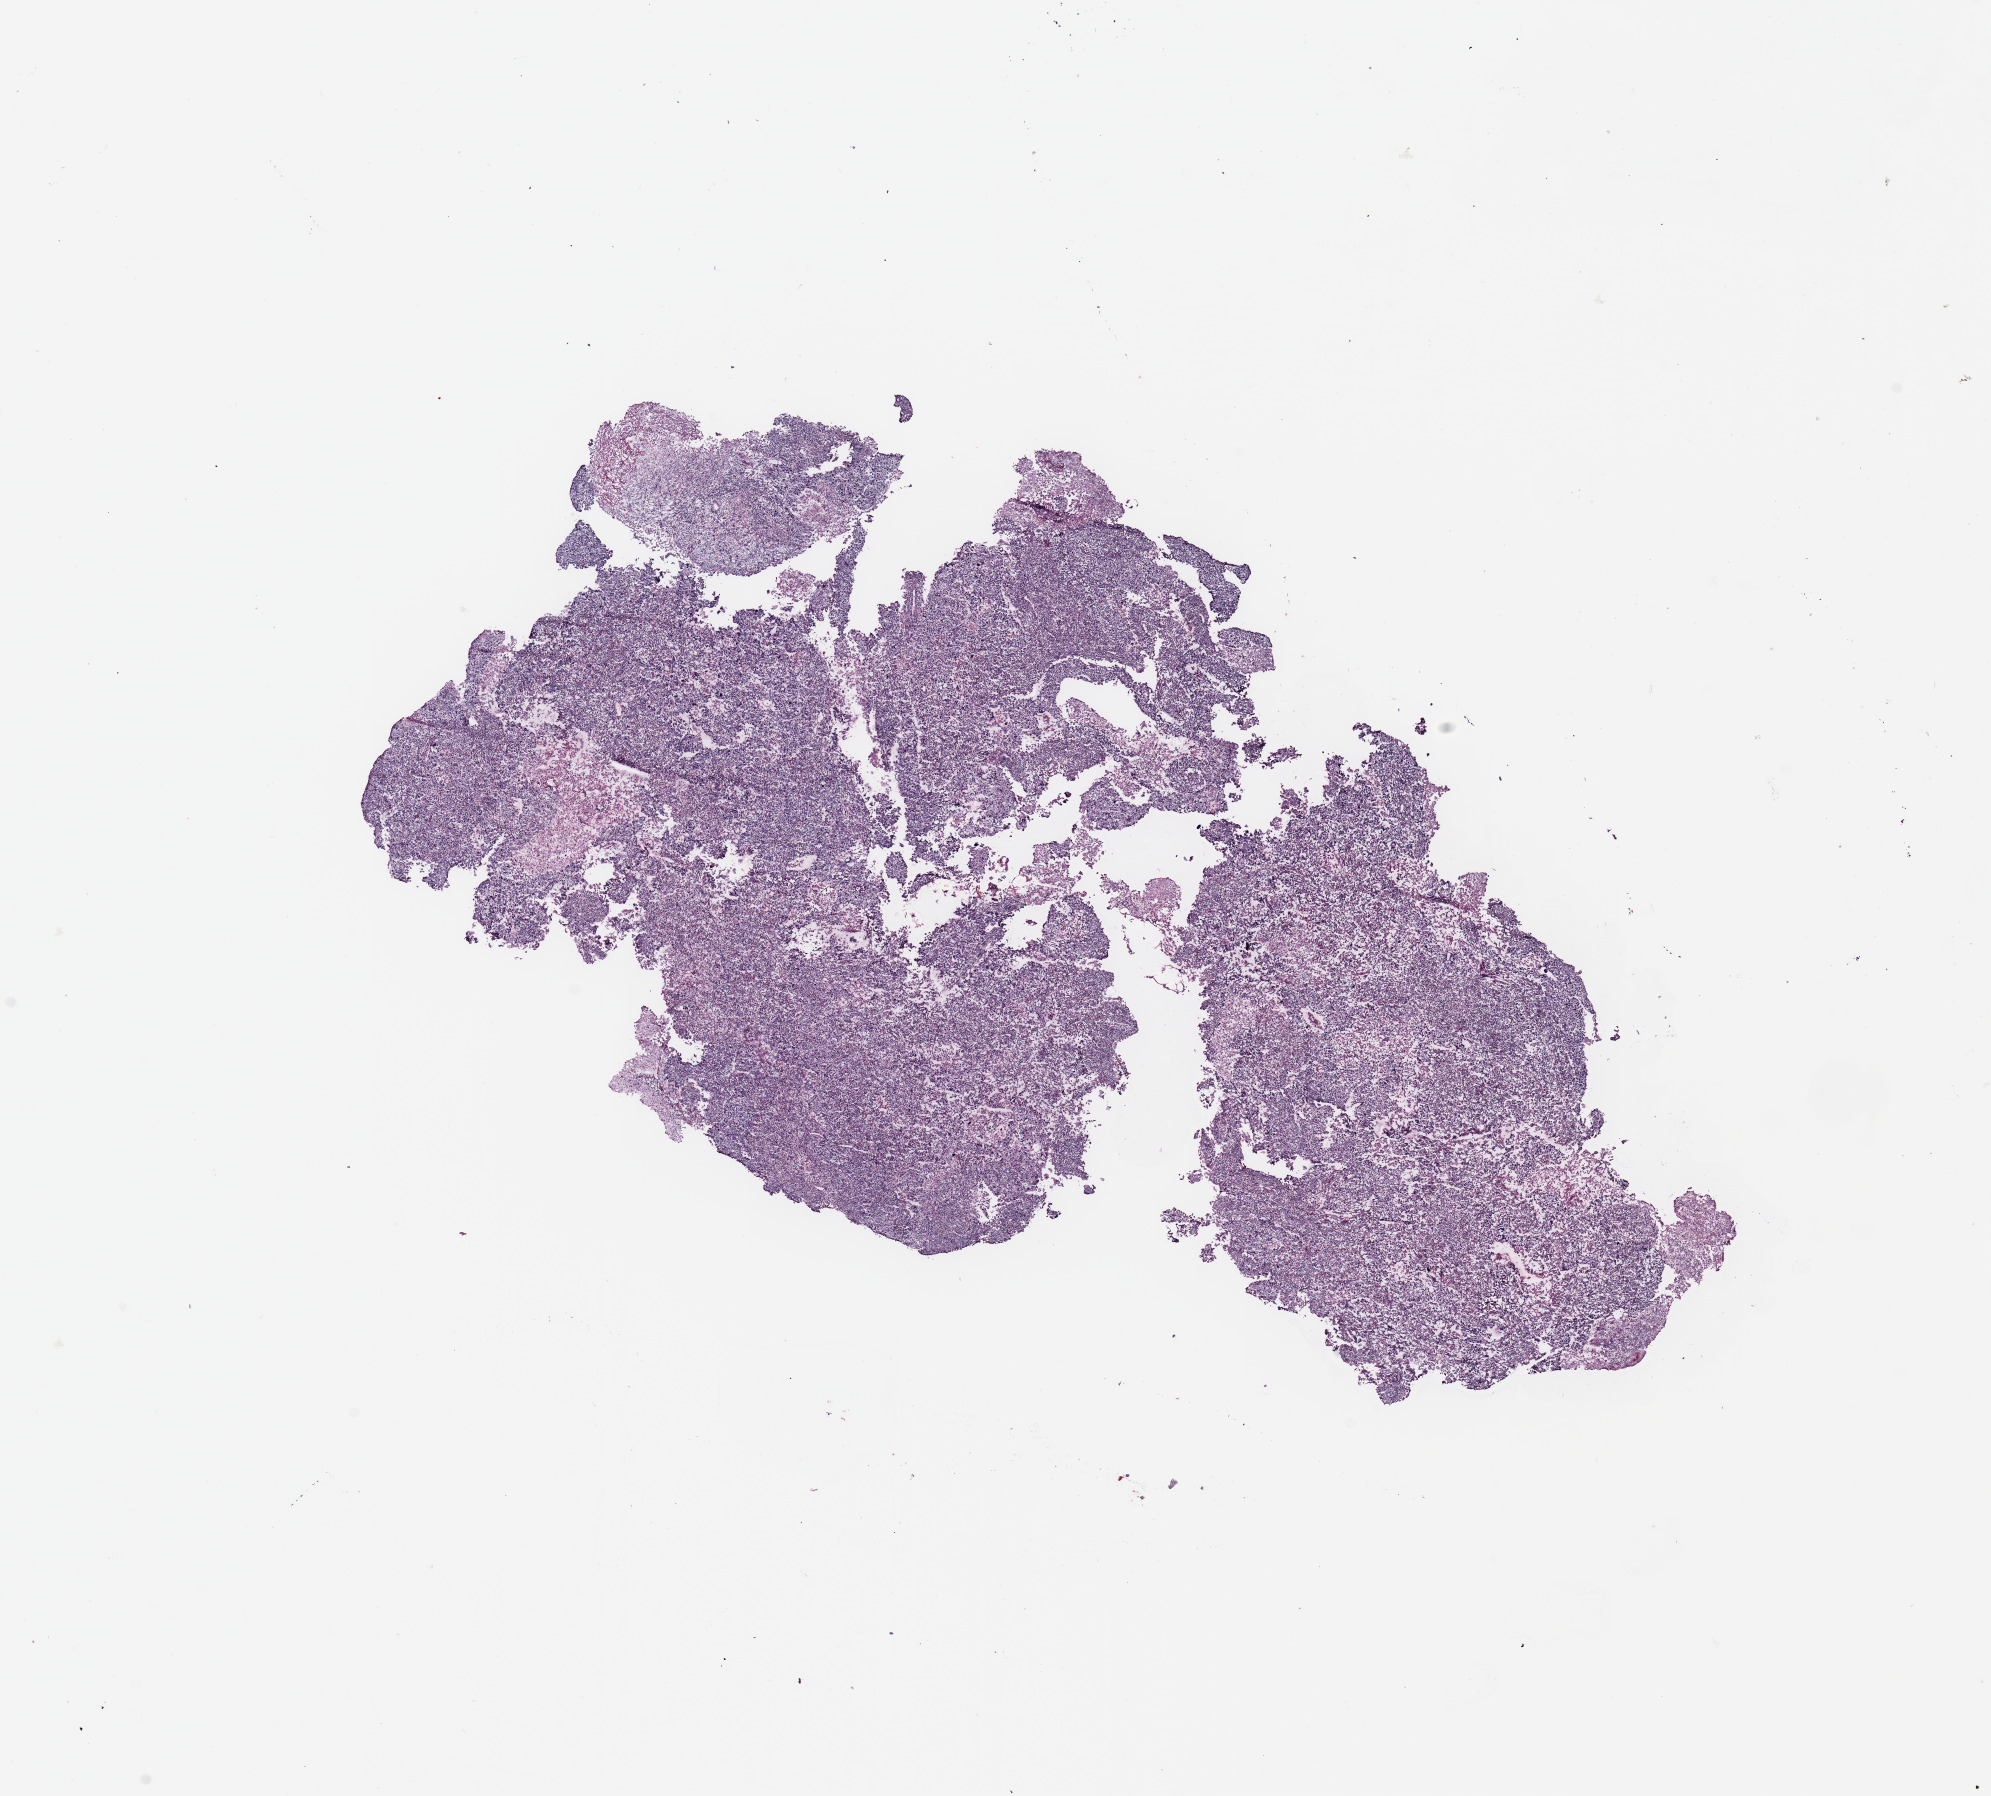
Digitized H&E tissue section (whole slide), a low-resolution overview of the entire scanned area, about 15.8 x 14.2 mm (slide scanned at 20x). Breast, tissue type not recorded.
• patient diagnosis (cohort enrolment): breast cancer (breast)